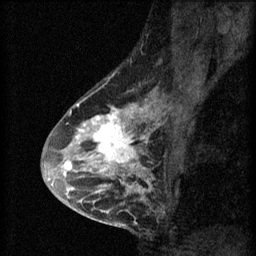
Breast MRI (dynamic contrast-enhanced), one sagittal slice. Slice 38 of 60 in the series (ordered by position). 3 images stored at this slice position (order not interpretable as contrast timing). 1.5 T. TE 4.2 ms, TR 8.2 ms. 2 mm slice thickness. 256 × 256 image matrix, field of view 180 × 180 mm. Female patient, age 45 years.
Outlined on this slice (semi-automatic segmentation, software-assisted and operator-edited):
- analysis volume of interest (the breast-tissue region the enhancement analysis was run in; not a lesion): box from (x=54, y=104) to (x=157, y=217) px
- tumour enhancement mask (voxels above the 70 % enhancement threshold inside the analysis volume of interest): (x=54, y=104)–(x=153, y=213)